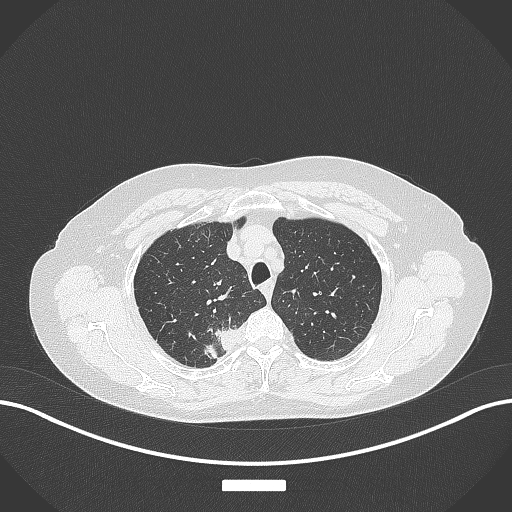
Chest CT, one axial slice; position 318 of 357 along the scan axis; reconstruction kernel B70f; 120 kVp; lung window (W 1500 / L -600 HU); 512 × 512 image matrix, field of view 400 × 400 mm. Patient: female, 62 years. Case-level facts recorded for this patient, not image findings: clinical TNM (as recorded): T1c N1 M0.
Outlined on this slice (rectangle marked by the reading radiologist):
- lung tumour (recorded histology: squamous cell carcinoma): bounding box <203,320,244,363> (left, top, right, bottom; pixels)